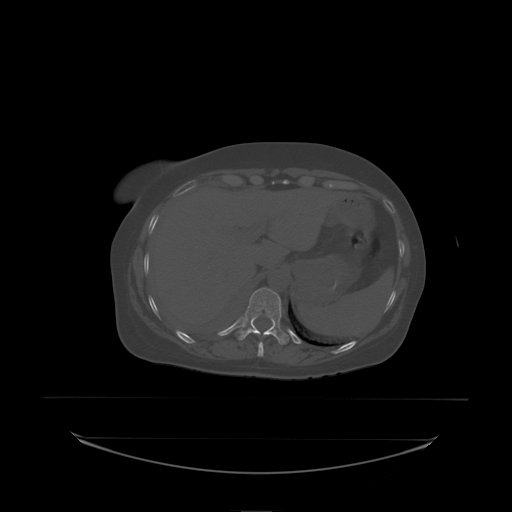
CT including the spine, one axial slice; bone window (W 1800 / L 400 HU); 2.5 mm slice thickness; 512 × 512 image matrix. Patient: female, 53 years. Case-level facts recorded for this patient, not image findings: primary cancer: lung.
Outlined on this slice (semi-automatic segmentation, software-assisted and operator-edited):
- T11 vertebra: bounding box [x1, y1, x2, y2] px = [237, 288, 284, 338]